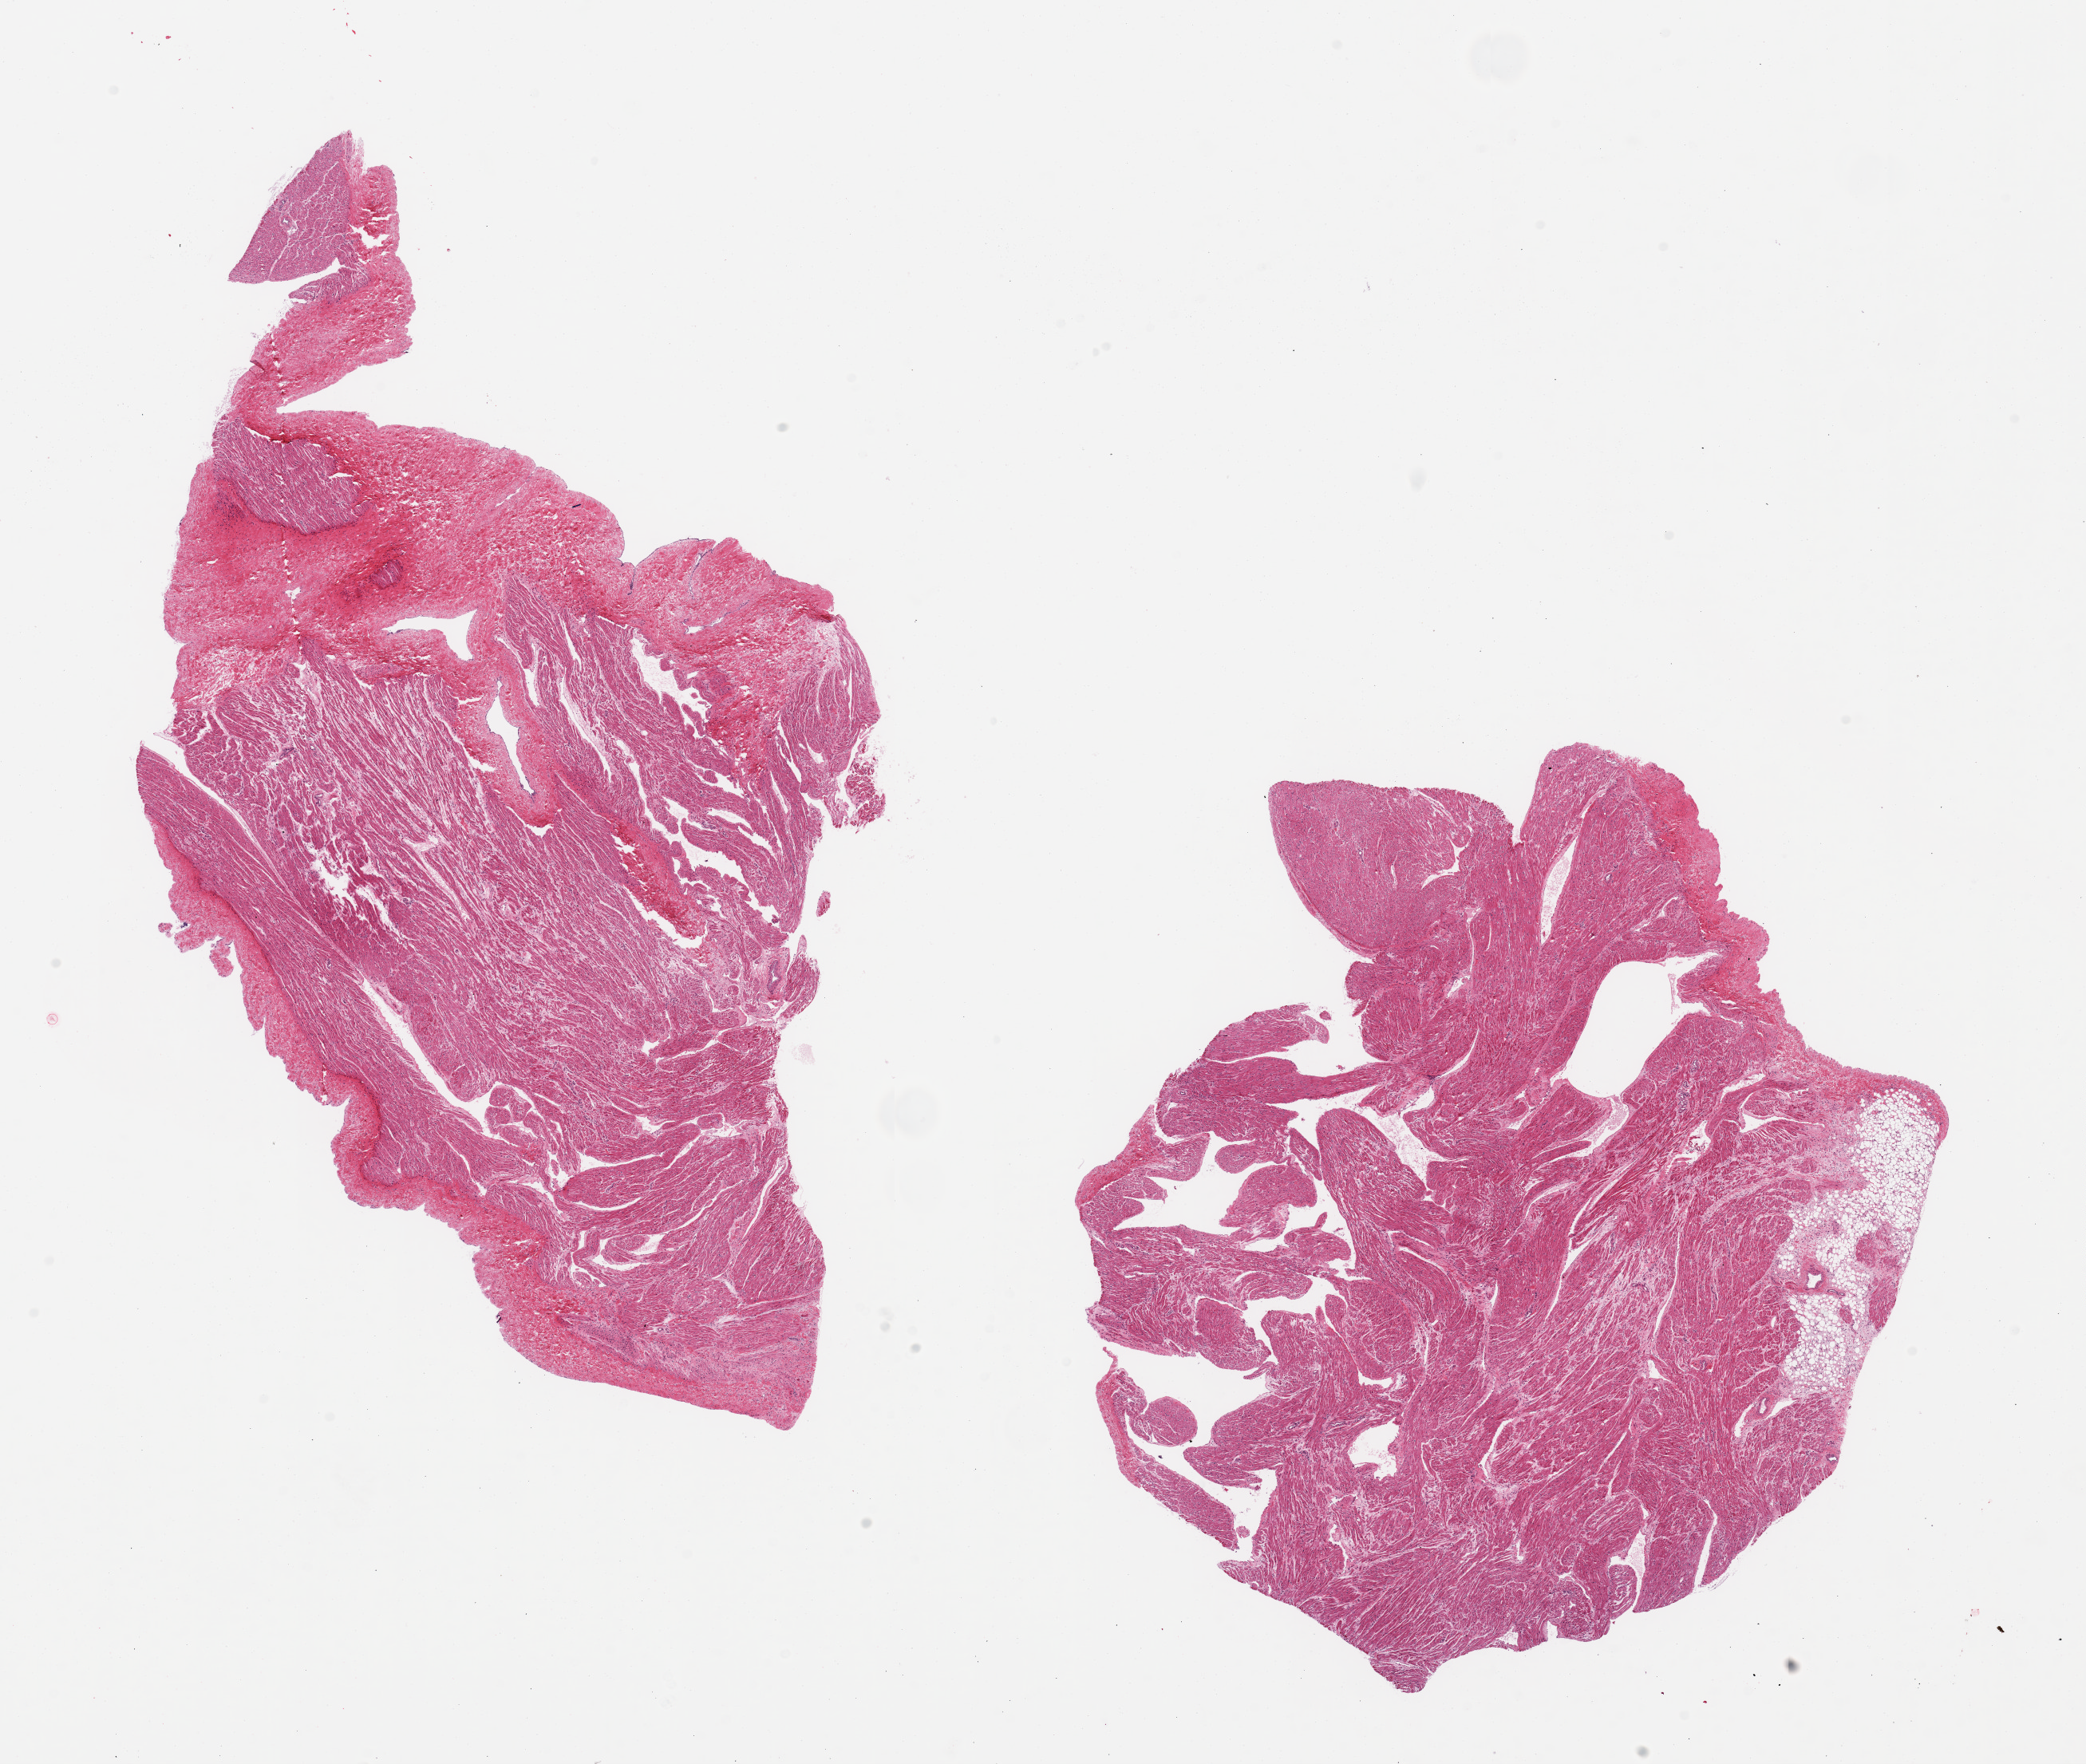
Whole-slide image, hematoxylin and eosin (H&E) stain, brightfield, whole scanned area (about 20.7 x 17.5 mm, slide scanned at 20x) shown as a low-resolution overview, PAXgene-fixed paraffin-embedded (PFPE) section, section of auricular appendage (target tissue), donor tissue sample. Female donor.
Reviewer comment on this tissue sample: 2 pieces, no abnormalities.